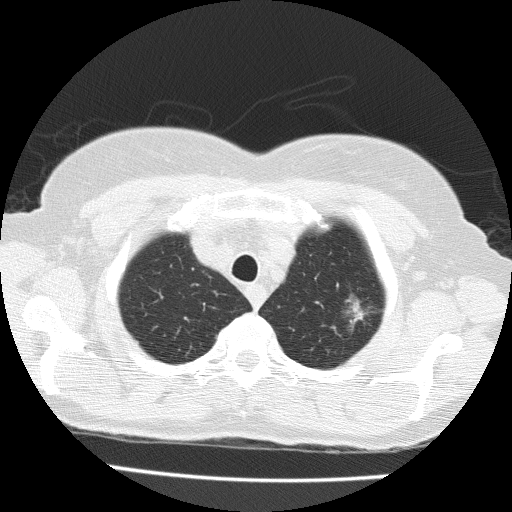
Axial slice from a low-dose chest CT screening exam; first (baseline) screen; lung window (W 1500 / L -600 HU); lung (sharp) reconstruction kernel (FC51); slice 26 of 183 in the series; 512 × 512 image matrix. Female, age 71 years at enrolment. Former smoker at enrolment.
- Expert reader's lesion annotation, bounding box (x1, y1, x2, y2) in pixels: (338, 291, 390, 337).
- Screening reader's record for this exam (one nodule recorded; not confirmed to be the boxed lesion): non-calcified nodule or mass ≥4 mm, left upper lobe, 15 × 10 mm, spiculated (stellate) margins, soft tissue attenuation.
- Official screen result: positive, change unspecified: nodule(s) >= 4 mm or enlarging nodule(s), mass(es), or other non-specific abnormalities suspicious for lung cancer.